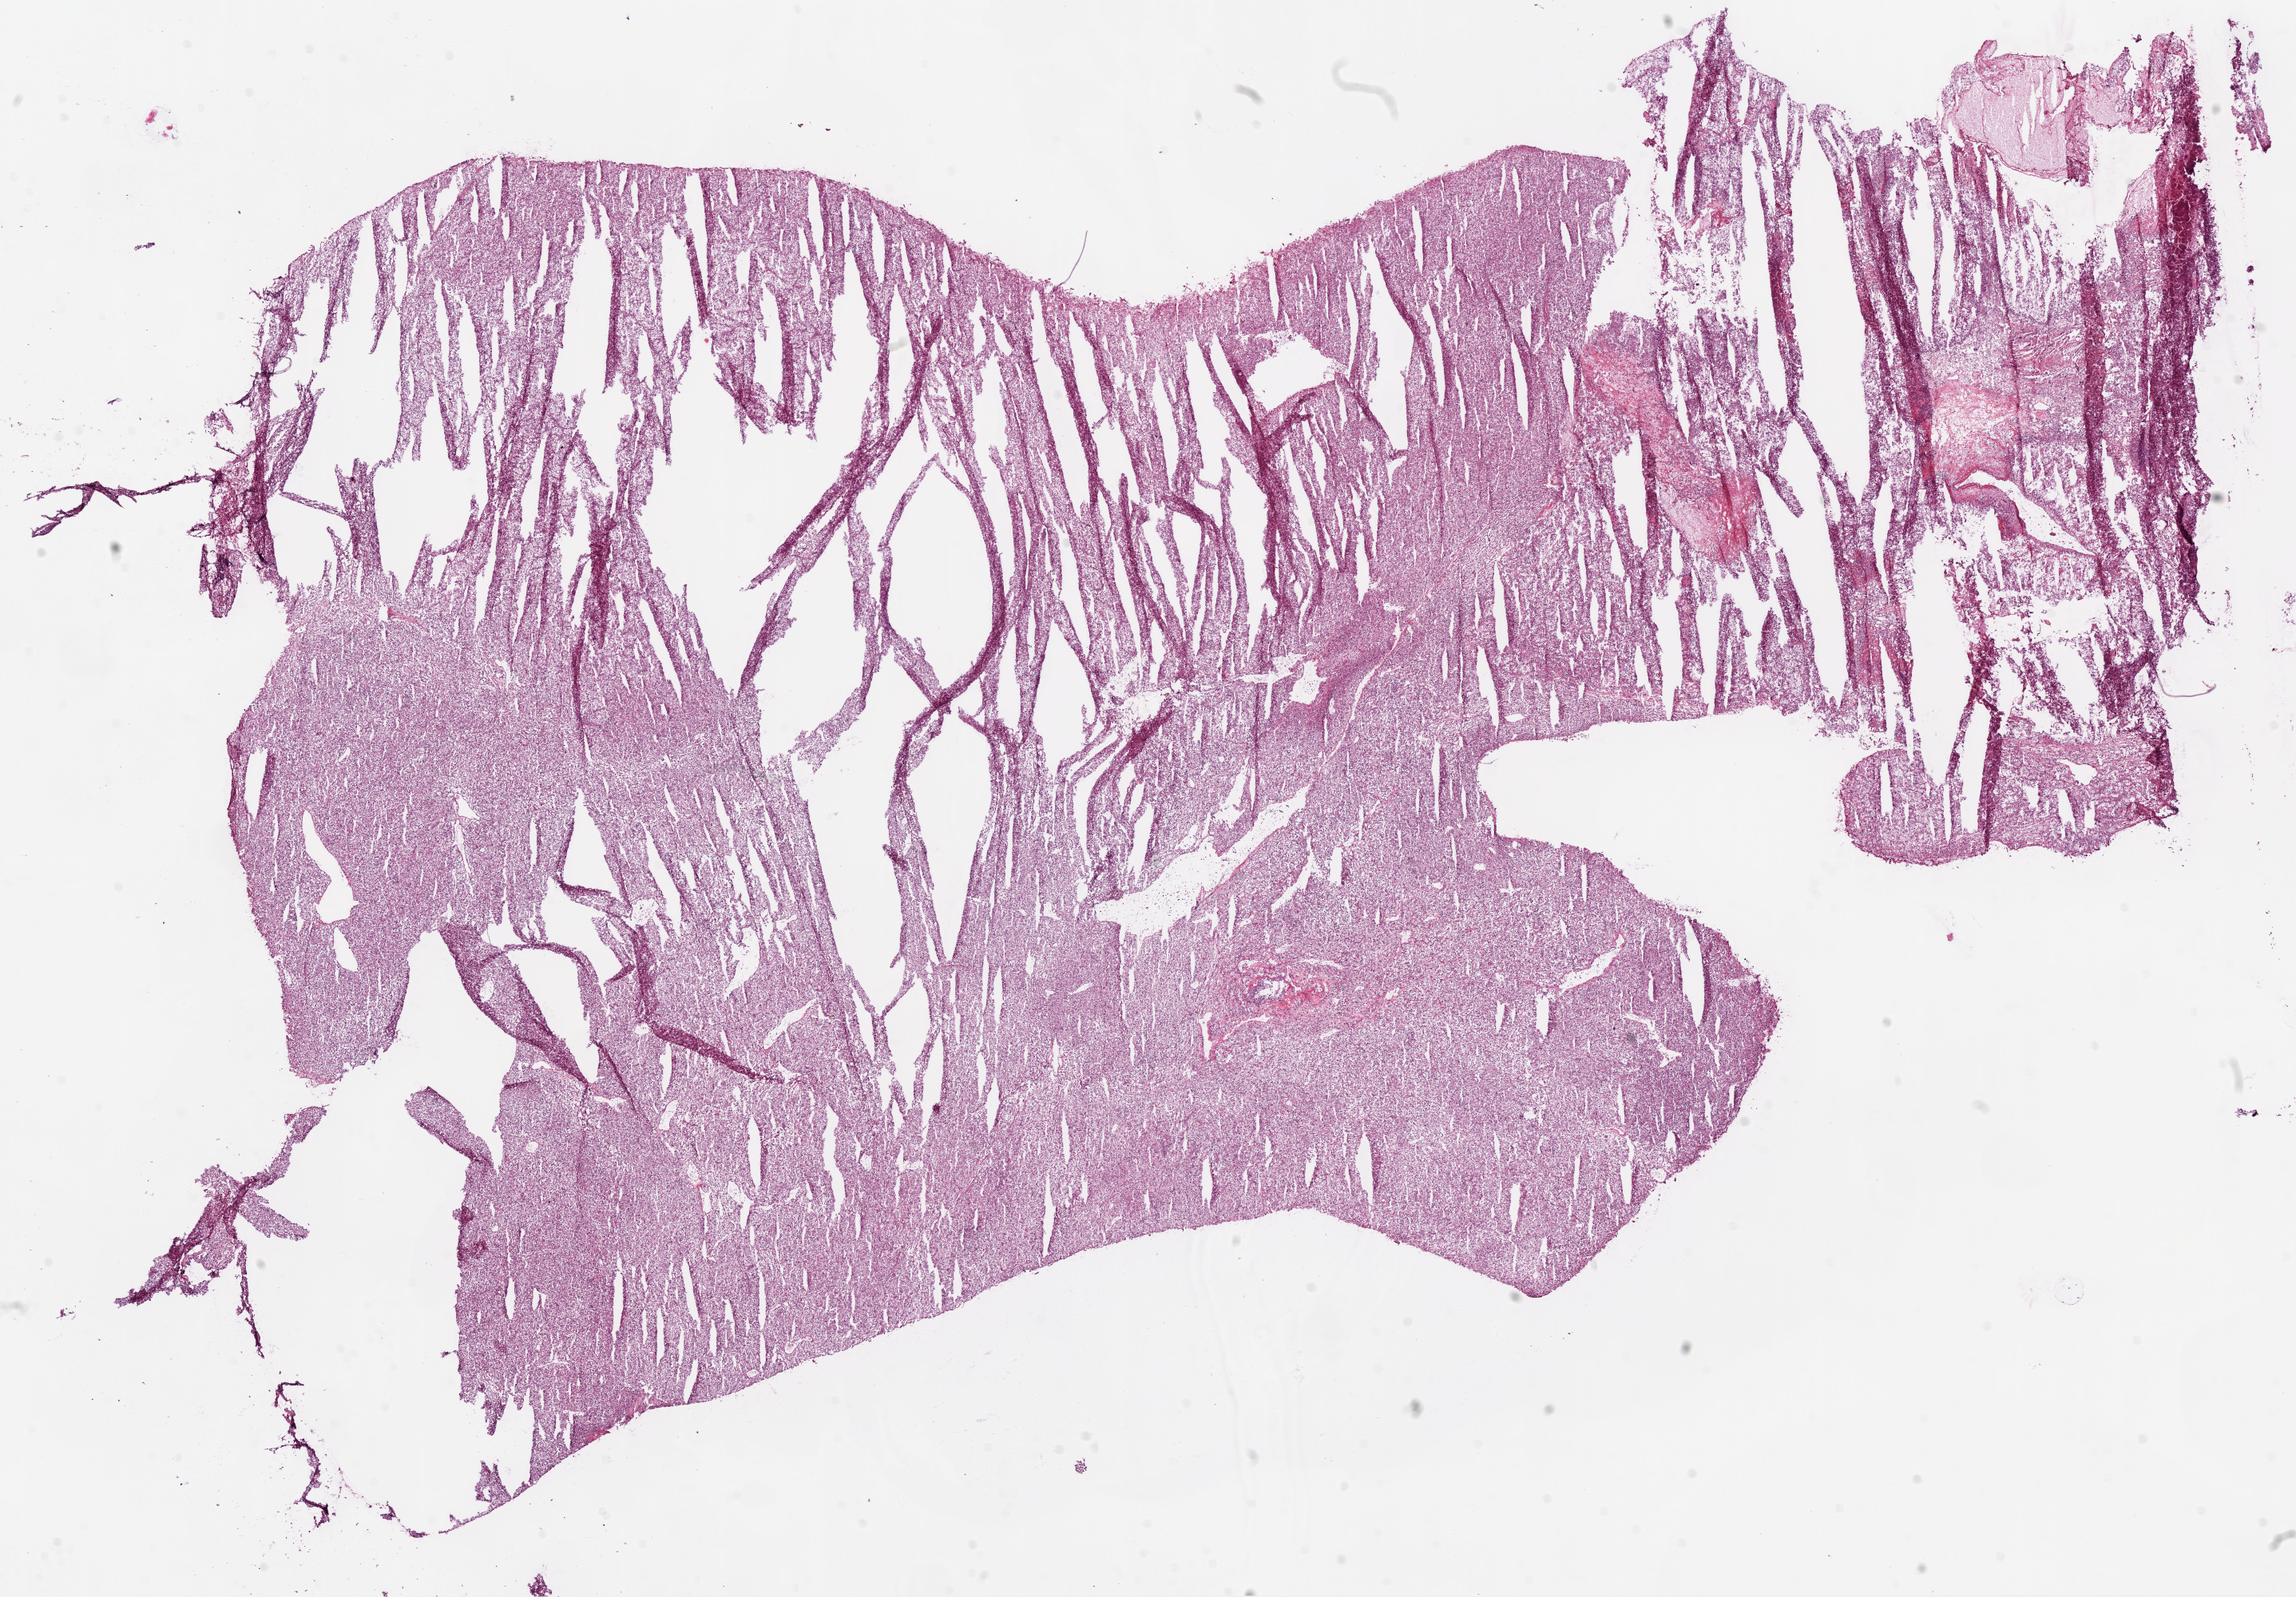
H&E whole-slide image, low-resolution overview of the scanned area, about 23.1 x 16.0 mm (from a 20x scan), frozen section, primary tumour sample from the kidney. Patient: male, age at initial diagnosis 74 years. Histologic grade: G3 (poorly differentiated). Slide review estimates, as recorded: tumour cells 95%, tumour nuclei 90%, normal cells 0%, stromal cells 5%, necrosis 0%.
Diagnosis: Clear cell adenocarcinoma, NOS. AJCC pathologic stage: I. Laterality: right.